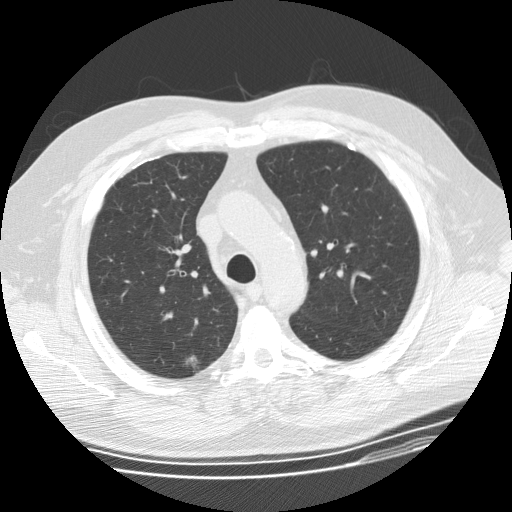
Axial slice from a low-dose chest CT screening exam. Third screening round (two years after baseline). Lung window (W 1500 / L -600 HU). 2.5 mm slice thickness. 512 × 512 image matrix, field of view 380 × 380 mm. Male, age 62 years at enrolment. Former smoker at enrolment.
Lesion marked by an expert reader, bounding box (x1, y1, x2, y2) in pixels: (167, 348, 212, 385). Screening reader's record for this exam (one nodule recorded; not confirmed to be the boxed lesion): non-calcified nodule or mass ≥4 mm, right upper lobe, 10 × 10 mm, poorly defined margins, ground glass attenuation, pre-existing on the prior screen: yes; interval growth: yes. Official screen result: positive, other. Lung cancer was diagnosed 48 days after this screen: bronchiolo-alveolar adenocarcinoma, NOS, right upper lobe, well differentiated (G1), stage IA (AJCC 6th edition), 12 mm at pathology.